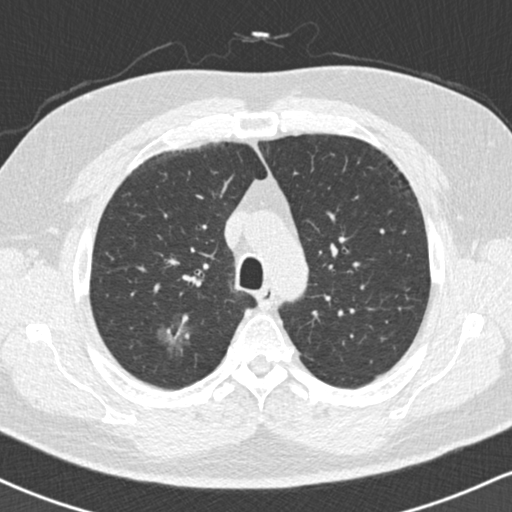
Chest CT (low-dose screening protocol), one axial image. Second annual screen. Lung window (W 1500 / L -600 HU). Standard (soft-tissue) reconstruction kernel (B30f). 120 kVp. Slice 45 of 169 in the series. 512 × 512 image matrix. Male, age 59 years at enrolment. Current smoker at enrolment.
Expert reader's lesion annotation, bounding box <153,305,208,361> (left, top, right, bottom; pixels). Screening reader's record for this exam (one nodule recorded; not confirmed to be the boxed lesion): non-calcified nodule or mass ≥4 mm, right upper lobe, 18 × 16 mm, ground glass attenuation, pre-existing on the prior screen: yes. Official screen result: positive, no significant change: stable abnormalities potentially related to lung cancer, unchanged since the prior screening exam. Later outcome: lung cancer diagnosed 60 days after this screen — bronchiolo-alveolar adenocarcinoma, NOS, right lower lobe, stage IA (AJCC 6th edition), 15 mm at pathology.